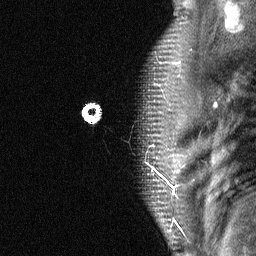
Breast MRI (dynamic contrast-enhanced), one sagittal slice. Position 53 of 64 along the scan axis. Dynamic contrast-enhanced study with each time point stored as its own series, time point 2 of 4 at this slice position (early post-contrast, ordered by acquisition time). 1.5 T. TE 4.8 ms, TR 27 ms. 2 mm slice thickness. 256 × 256 image matrix, field of view 180 × 180 mm. Patient: female, 50 years. From the clinical record (not read from this slice): setting: breast cancer imaged before/during neoadjuvant chemotherapy; receptor status: HER2-positive.
Outlined on this slice (semi-automatically segmented with operator editing):
- analysis volume of interest (the breast-tissue region the enhancement analysis was run in; not a lesion): box from (x=139, y=91) to (x=189, y=177) px
- tumour enhancement mask (voxels above the 90 % enhancement threshold inside the analysis volume of interest): (x=152, y=167)–(x=154, y=170)